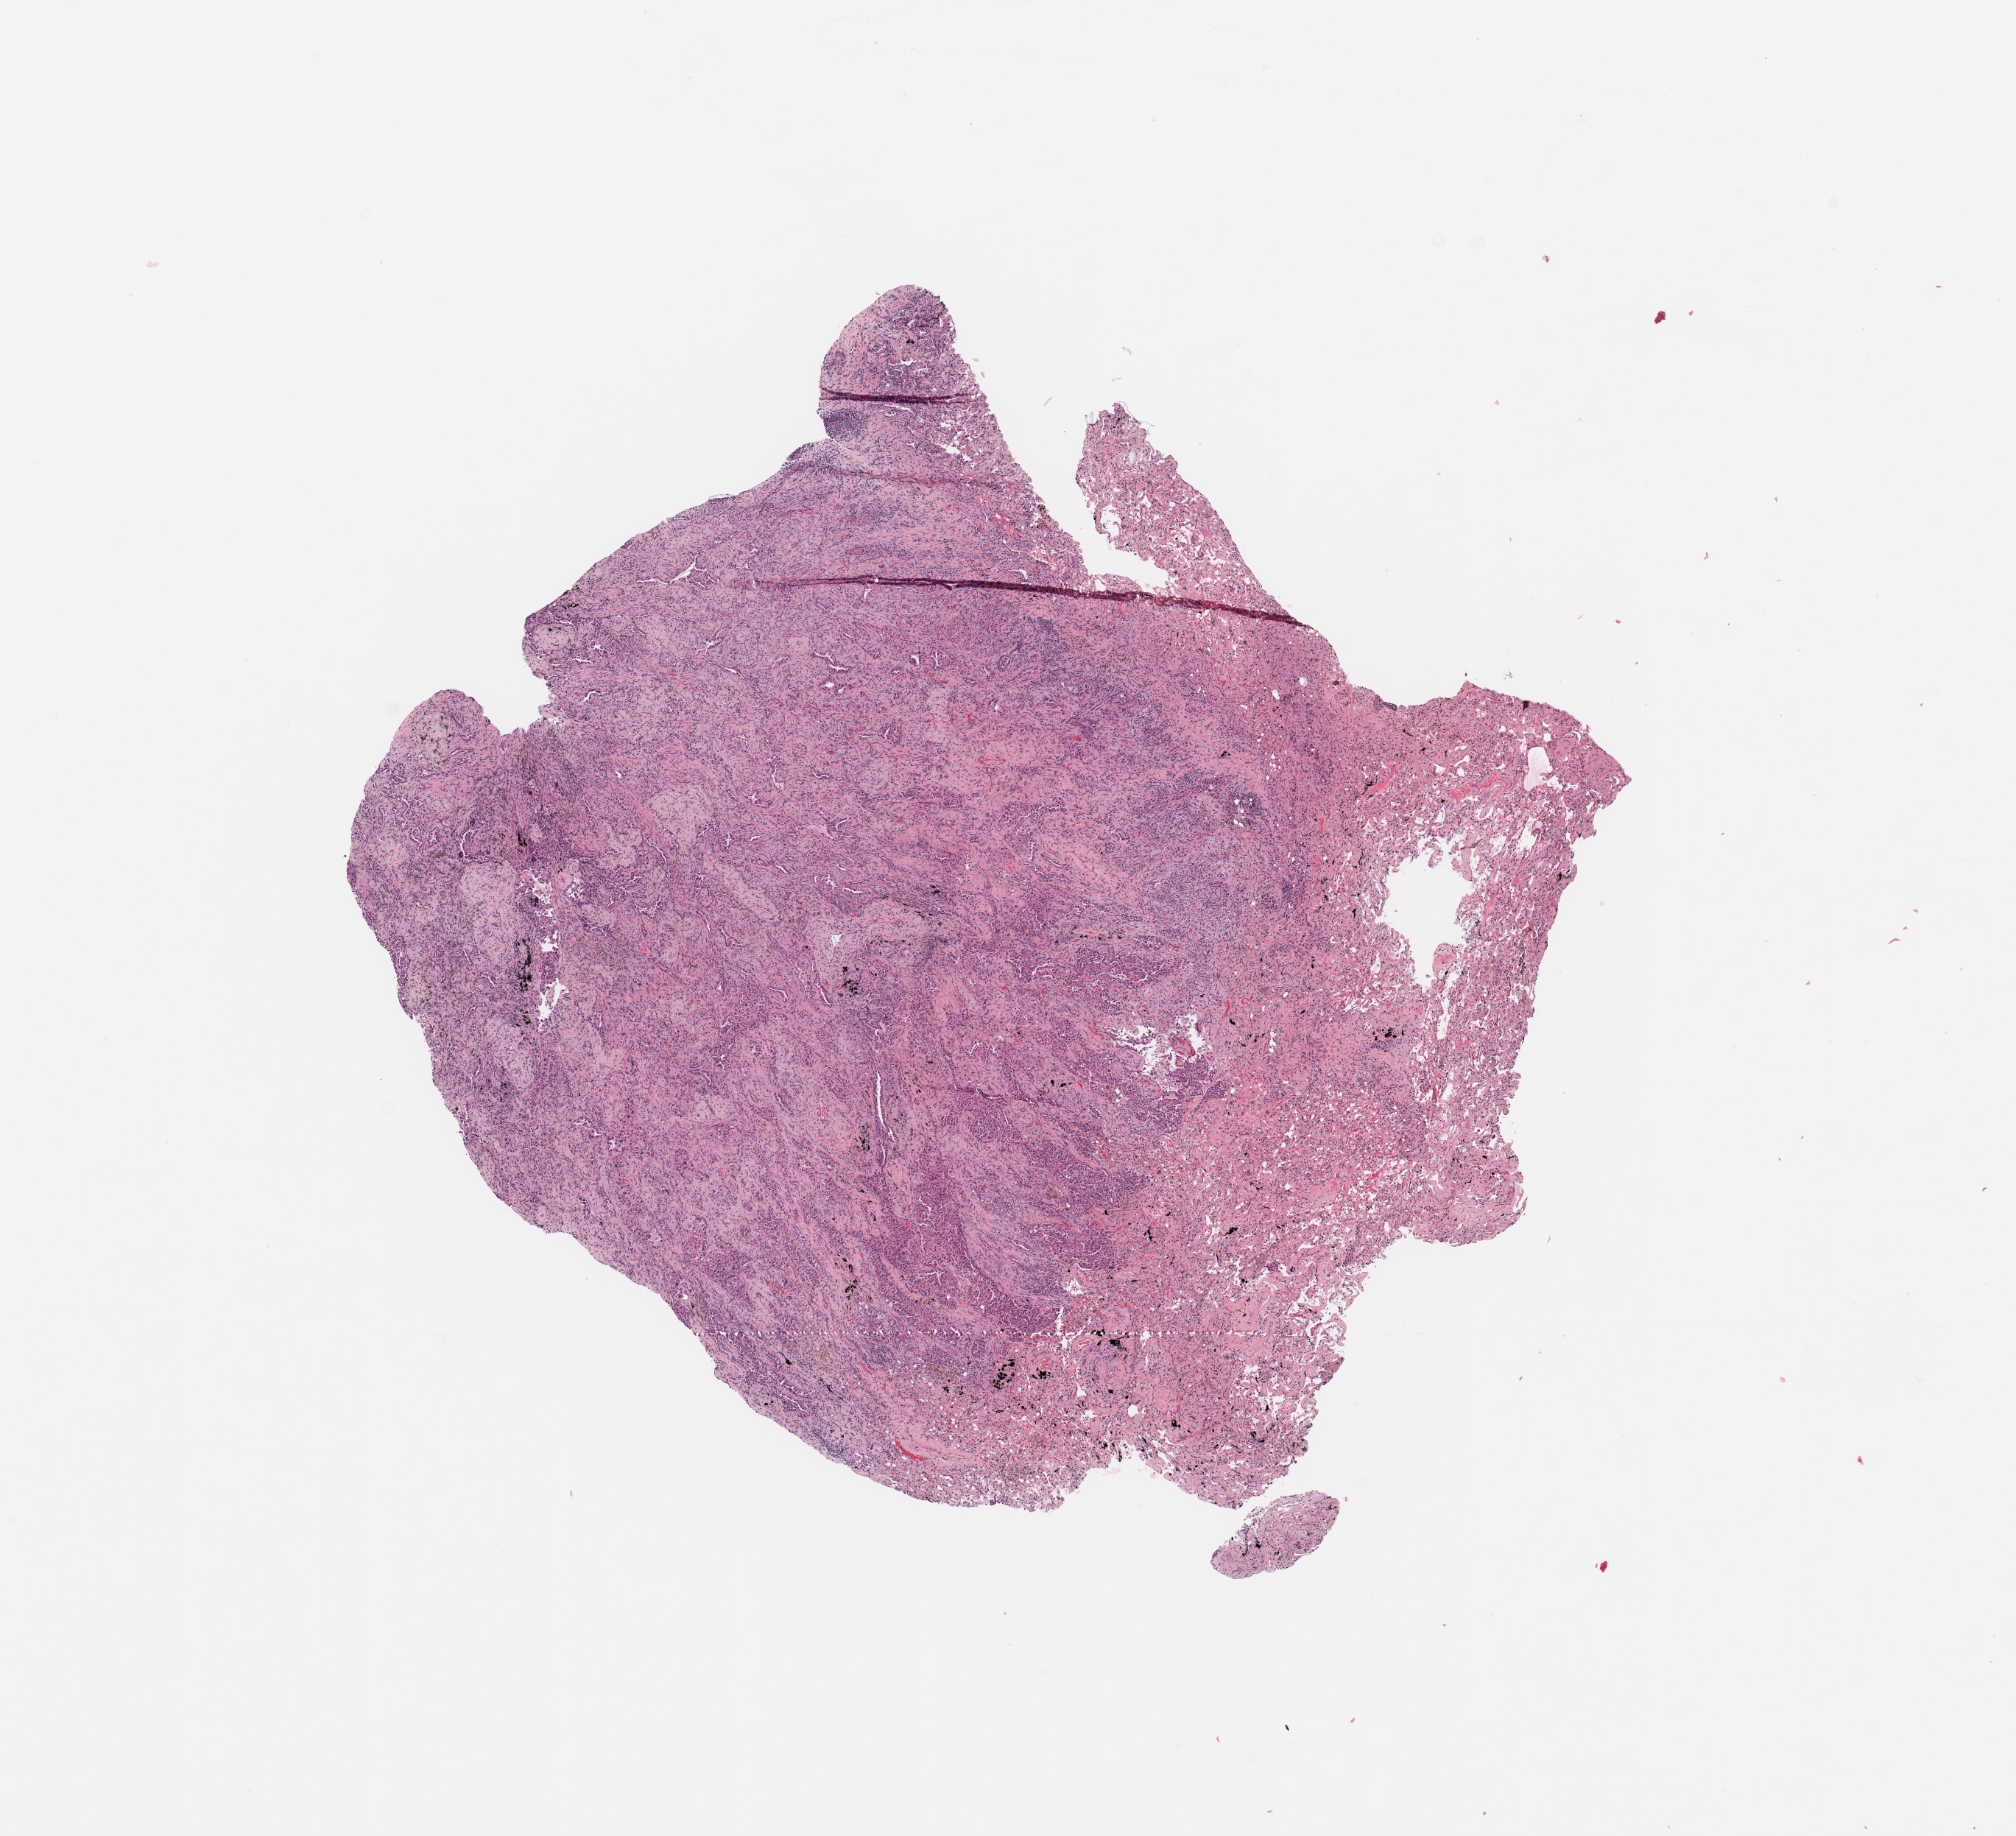
Hematoxylin and eosin (H&E) stained whole-slide image, whole scanned area (about 10.8 x 9.9 mm, from a 20x scan) shown as a low-resolution overview, tumour tissue sample, sampled site: lung. Male, 61 y/o. Slide review estimates, as recorded: tumour nuclei 65%, necrosis 2%.
Histologic diagnosis: Adenocarcinoma, NOS.